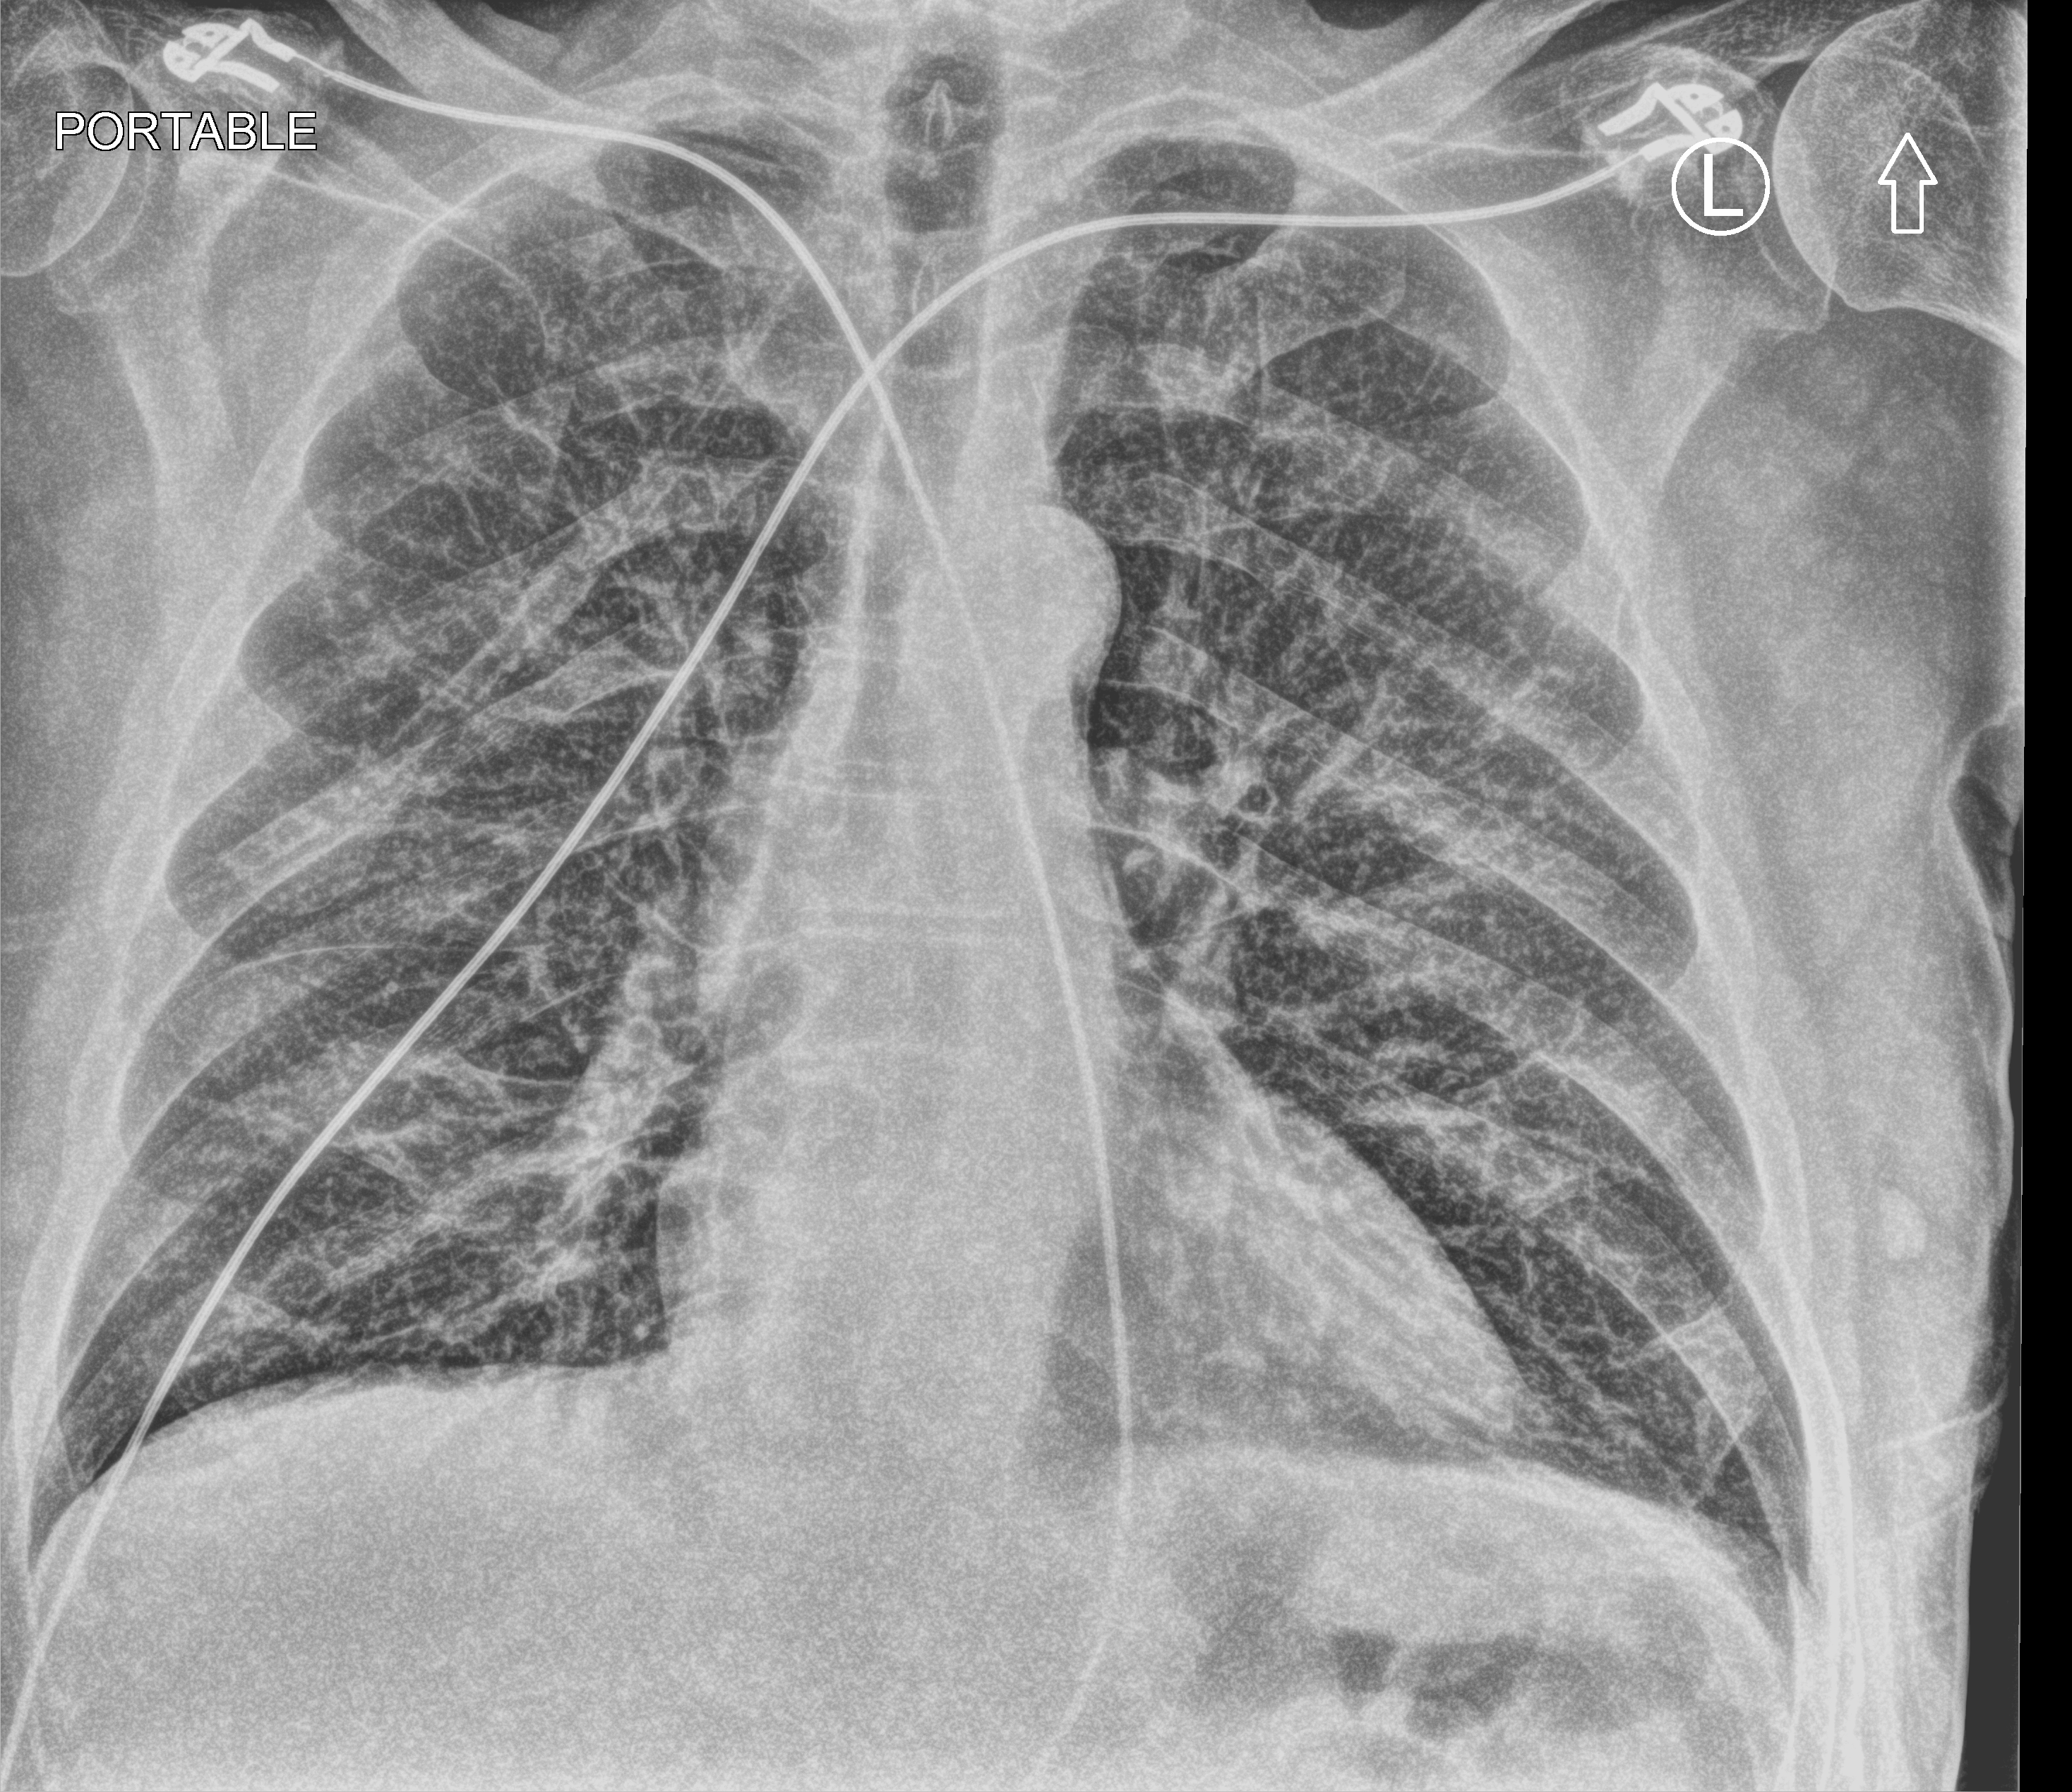
Portable chest radiograph; anteroposterior (AP) projection. Male patient hospitalised with COVID-19, age 60–74 years.
Admission-level facts for this patient (not findings on this image; timing relative to this image not recorded): other chronic lung disease (admission record): no; mechanically ventilated during this hospital stay: no; COPD (admission record): yes.